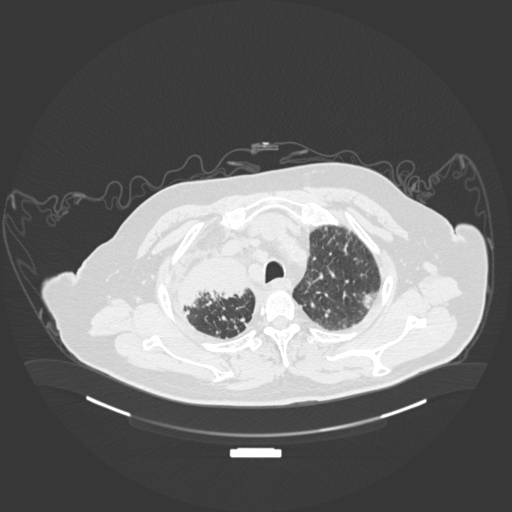
Chest CT, one axial slice. Slice 155 of 201 in the series (ordered by position). Reconstruction kernel B30f. 120 kVp. Lung window (W 1500 / L -600 HU). 1 mm slice thickness. 512 × 512 image matrix, field of view 500 × 500 mm. Patient: male, 69 years. Case-level facts recorded for this patient, not image findings: clinical TNM (as recorded): T4 N3 M1.
Structures marked on this image (bounding box drawn by a radiologist):
- lung tumour (recorded histology: adenocarcinoma): bounding box <170,252,256,317> (left, top, right, bottom; pixels)